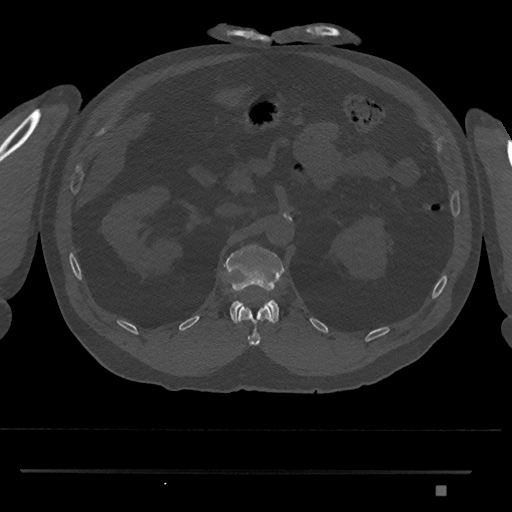
CT including the spine, one axial slice. Slice 854 of 1134 in the series (ordered by position). Reconstruction kernel Br40s/3. Bone window (W 1800 / L 400 HU). 0.5 mm slice thickness. 512 × 512 image matrix. Patient: male, 65 years. Case-level facts recorded for this patient, not image findings: primary cancer: prostate.
Structures marked on this image (semi-automatically segmented with operator editing):
- L1 vertebra: bounding box [x1, y1, x2, y2] px = [223, 244, 285, 324]
- T12 vertebra: [237, 303, 274, 346]